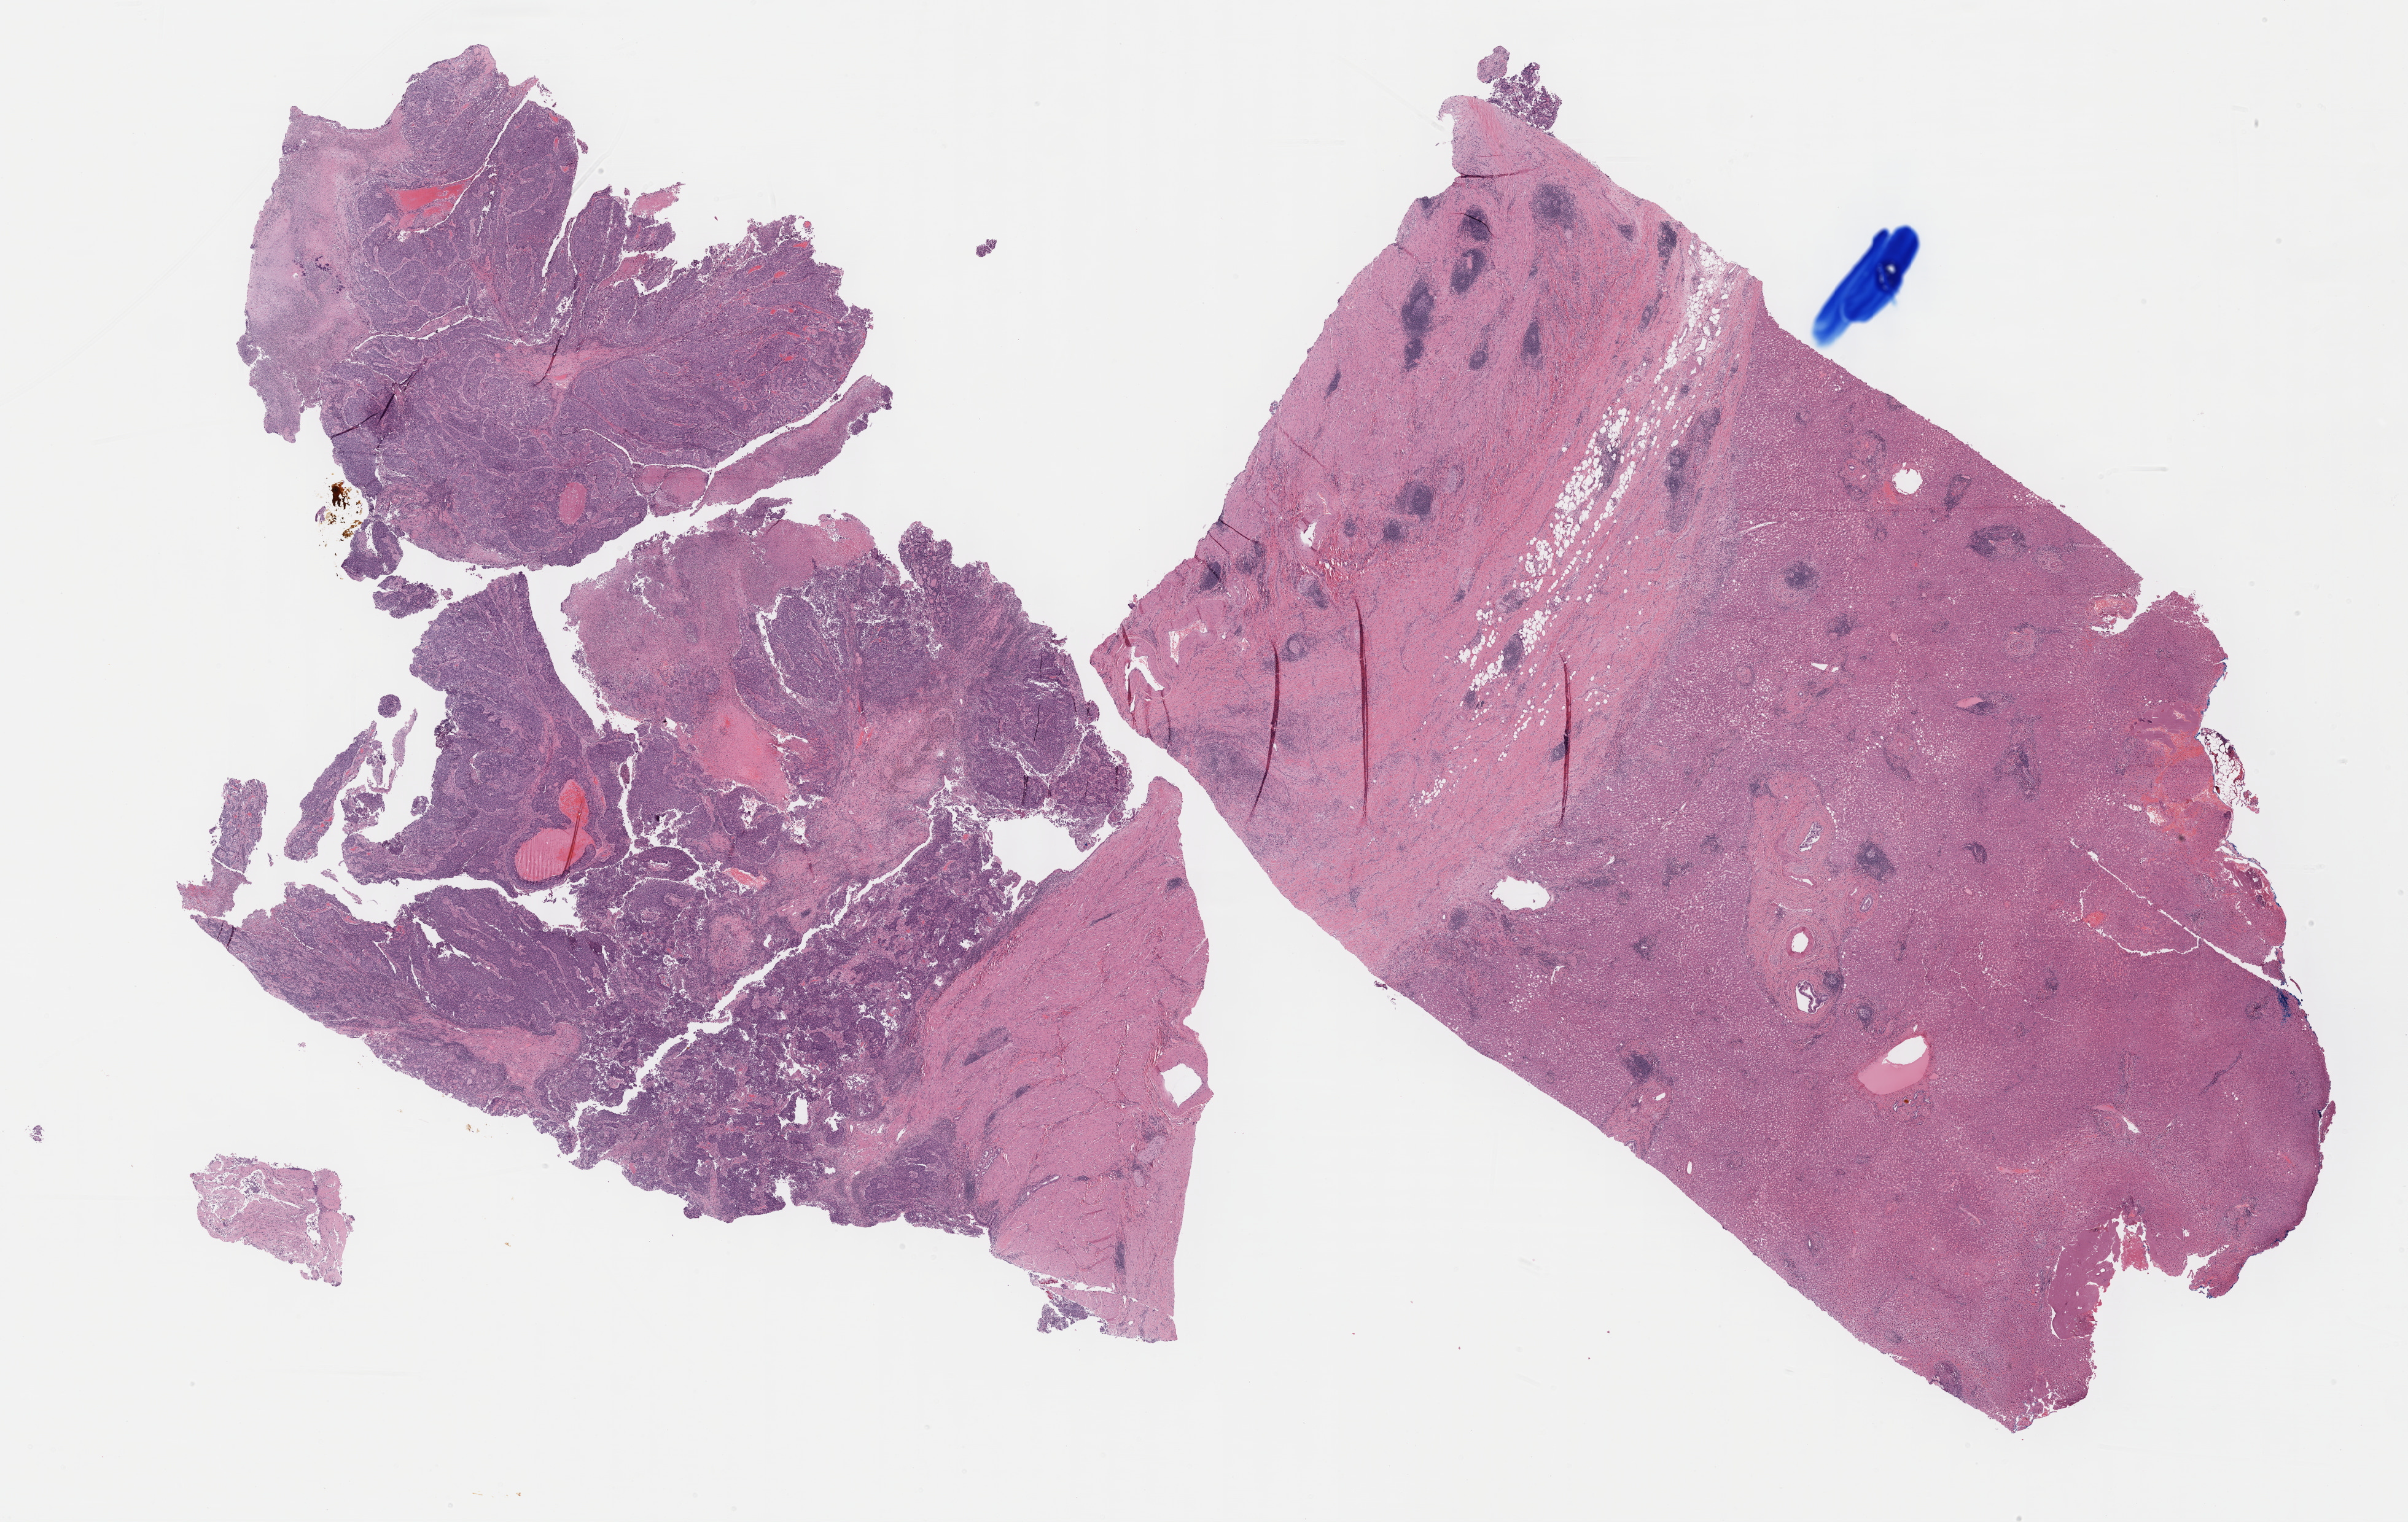
Digitized Hematoxylin and eosin (H&E) stained tissue section (whole slide), low-resolution overview of the scanned area, about 31.7 x 20.0 mm; formalin-fixed paraffin-embedded (FFPE) diagnostic section; primary tumour sample from the bile duct. Female, age 72 years at initial diagnosis. Histologic grade: G3 (poorly differentiated).
- AJCC pathologic stage: I
- histologic diagnosis: Cholangiocarcinoma (extrahepatic bile duct)